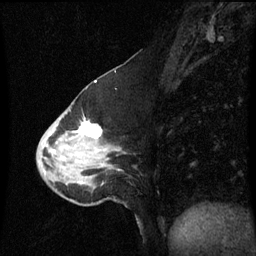
Breast MRI (dynamic contrast-enhanced), one sagittal slice; slice 26 of 60 in the series (ordered by position); dynamic contrast-enhanced series, image 2 of 3 at this slice position (ordered by acquisition); 1.5 T; TE 4.2 ms, TR 8.9 ms; 2 mm slice thickness; 256 × 256 image matrix, field of view 200 × 200 mm. Patient: female, 50 years. From the clinical record (not read from this slice): setting: breast cancer imaged before/during neoadjuvant chemotherapy; receptor status: HR-positive, HER2-negative.
Structures marked on this image (semi-automatically segmented with operator editing):
- analysis volume of interest (the breast-tissue region the enhancement analysis was run in; not a lesion): box from (x=38, y=90) to (x=123, y=207) px
- tumour enhancement mask (voxels above the 70 % enhancement threshold inside the analysis volume of interest): (x=80, y=124)–(x=103, y=139)